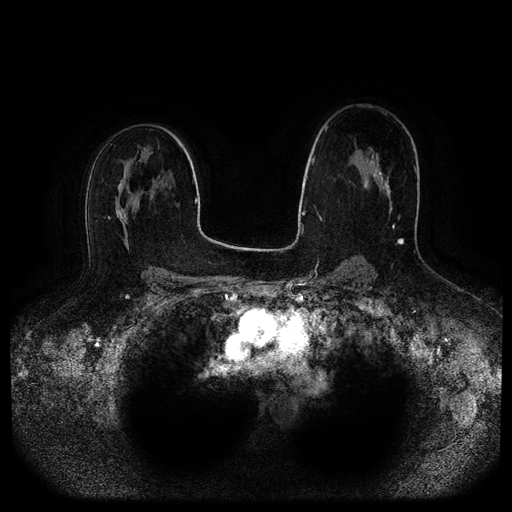
Breast MRI (dynamic contrast-enhanced, multi-phase), one axial slice; position 60 of 116 along the scan axis; dynamic contrast-enhanced series, time point 2 of 5 at this slice position (early post-contrast); 1.5 T; TE 2.6 ms, TR 5.2 ms; 2 mm slice thickness; 512 × 512 image matrix, field of view 380 × 380 mm. Female patient, age 45 years.
Outlined on this slice (semi-automatically segmented with operator editing):
- breast lesion (labelled benign in the annotation): box from (x=363, y=180) to (x=368, y=189) px